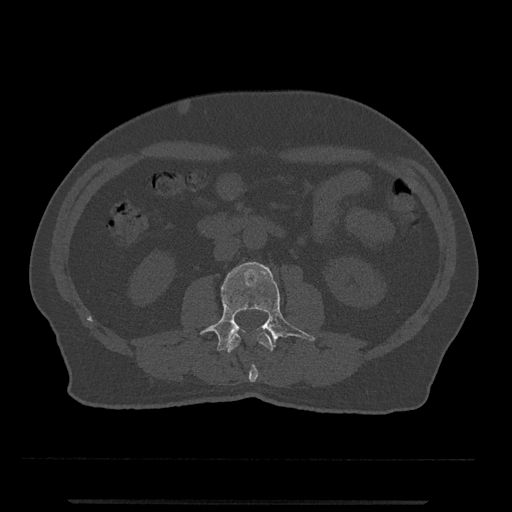
CT including the spine, one axial slice; slice 216 of 797 in the series (ordered by position); reconstruction kernel Br40s/3; 120 kVp; bone window (W 1800 / L 400 HU); 512 × 512 image matrix, field of view 419 × 419 mm. Patient: male, 63 years. From the clinical record (not read from this slice): primary cancer: prostate.
Outlined on this slice (semi-automatic segmentation, software-assisted and operator-edited):
- L2 vertebra: bounding box <227,332,273,382> (left, top, right, bottom; pixels)
- L3 vertebra: <200,262,315,352>